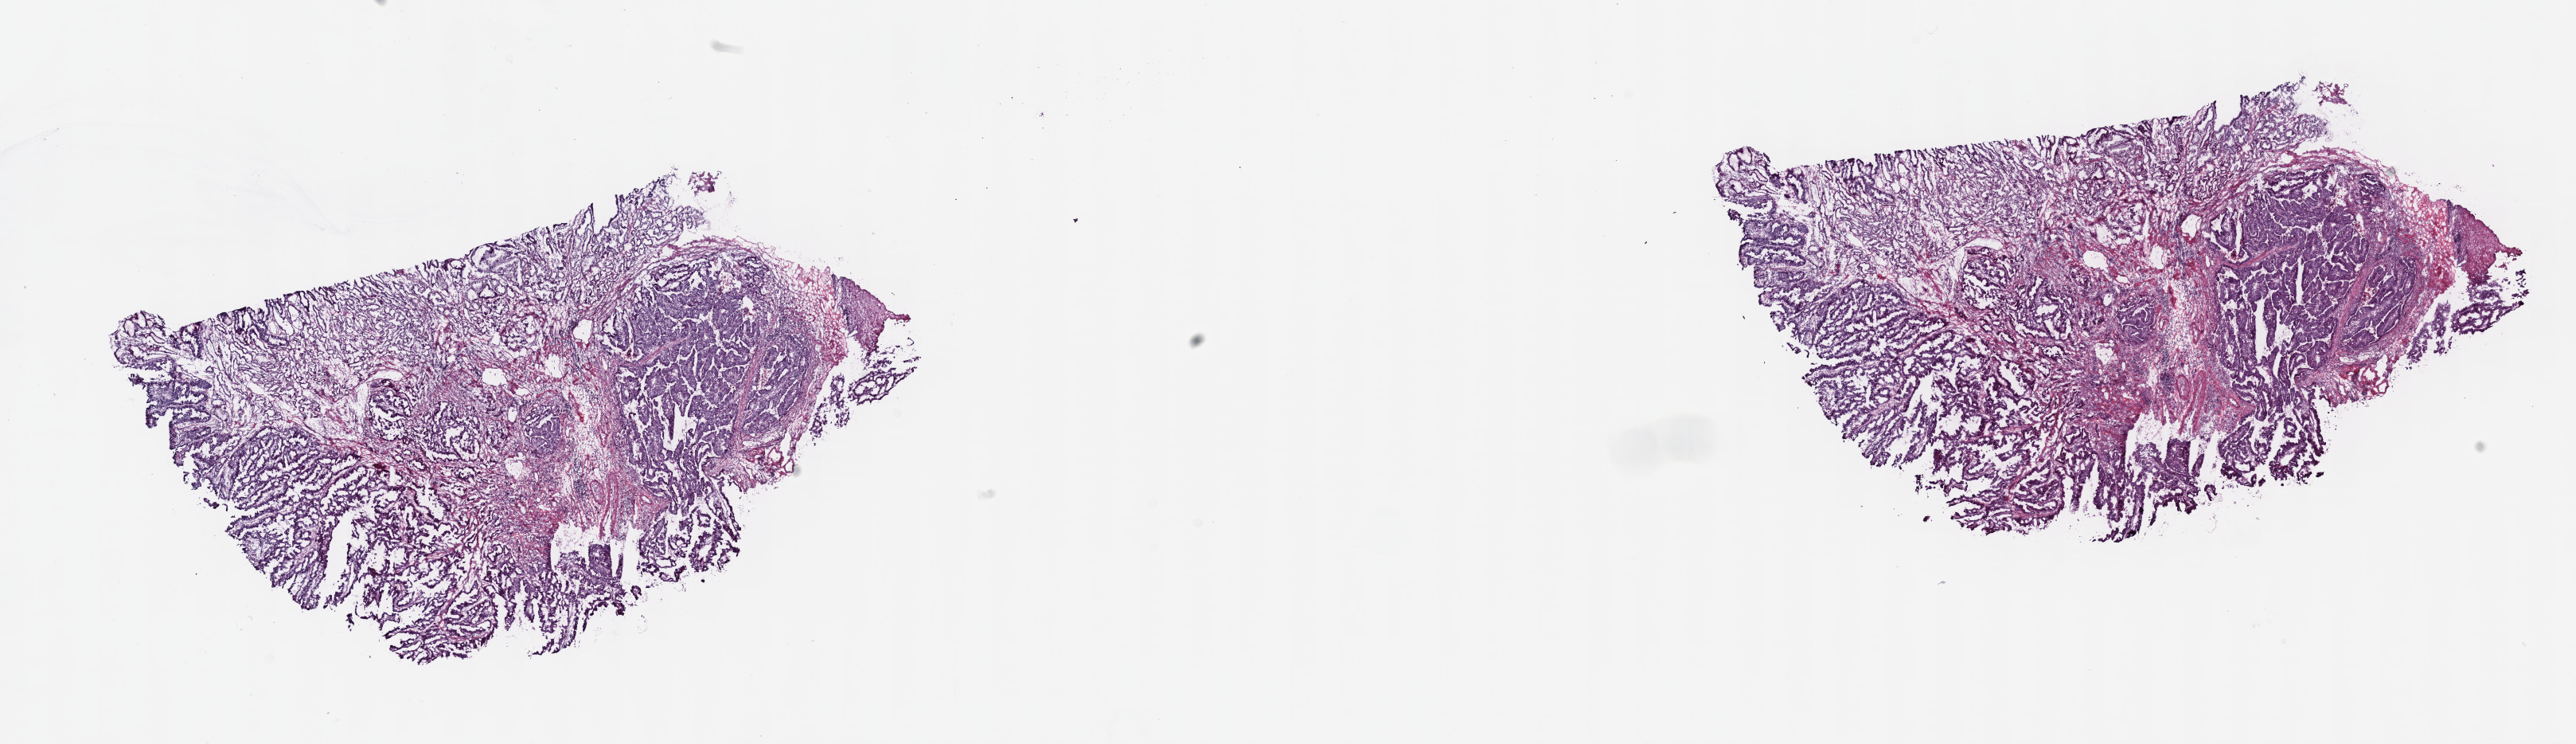
Whole-slide histology image, H&E — a low-resolution overview of the entire scanned area, about 26.2 x 7.6 mm, frozen section, esophagus, primary tumour sample. Patient: male, age at initial diagnosis 60 years.
Diagnosis: Adenocarcinoma, NOS (lower third of esophagus).